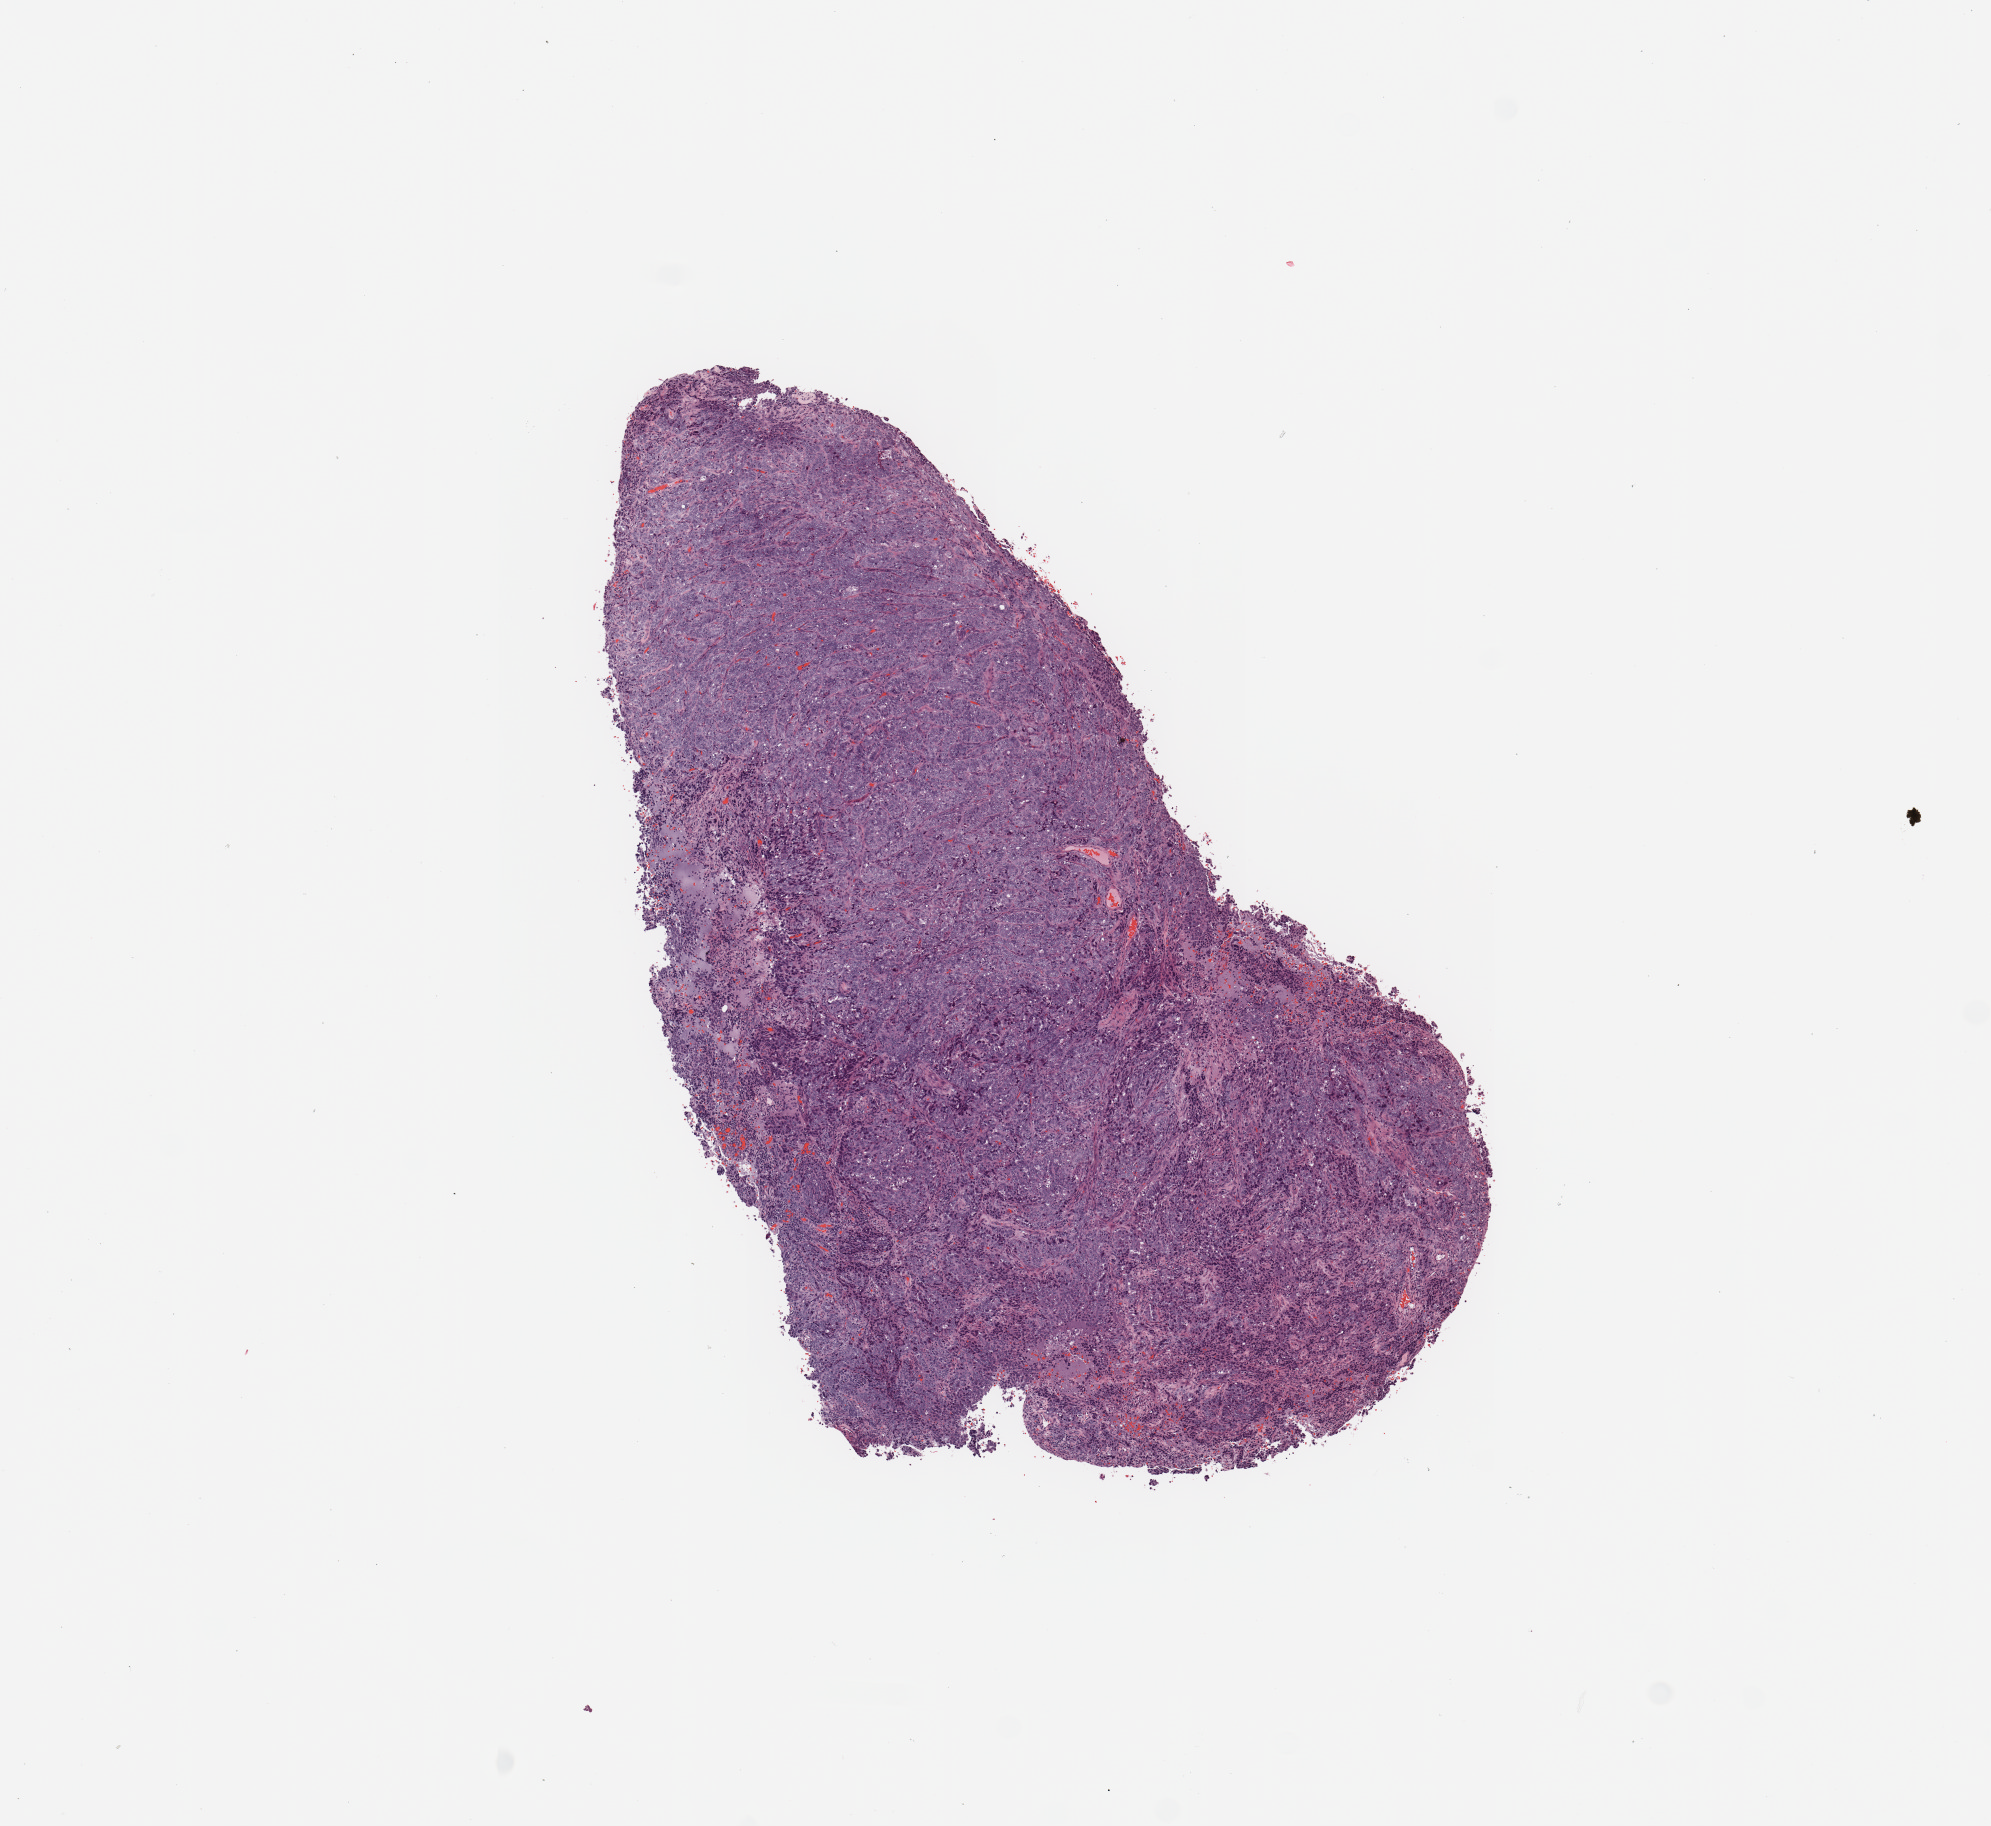
Whole-slide histology image, H&E-stained, a low-resolution overview of the entire scanned area, about 7.9 x 7.2 mm (slide scanned at 20x); tumour tissue sample, uterus. Patient: female, age 68 years. Histologic grade: G3 (poorly differentiated).
- AJCC pathologic stage: III
- histologic diagnosis: Endometrioid adenocarcinoma, NOS